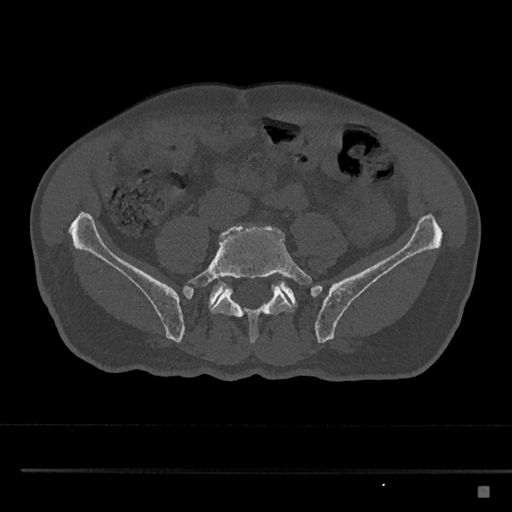
CT including the spine, one axial slice; slice 575 of 797 in the series (ordered by position); reconstruction kernel Br40s/3; bone window (W 1800 / L 400 HU); 0.5 mm slice thickness; 512 × 512 image matrix, field of view 391 × 391 mm. Patient: male, 59 years. Case-level facts recorded for this patient, not image findings: primary cancer: prostate.
Annotated regions visible in this slice (semi-automatic segmentation, software-assisted and operator-edited):
- L5 vertebra: box from (x=183, y=224) to (x=312, y=343) px